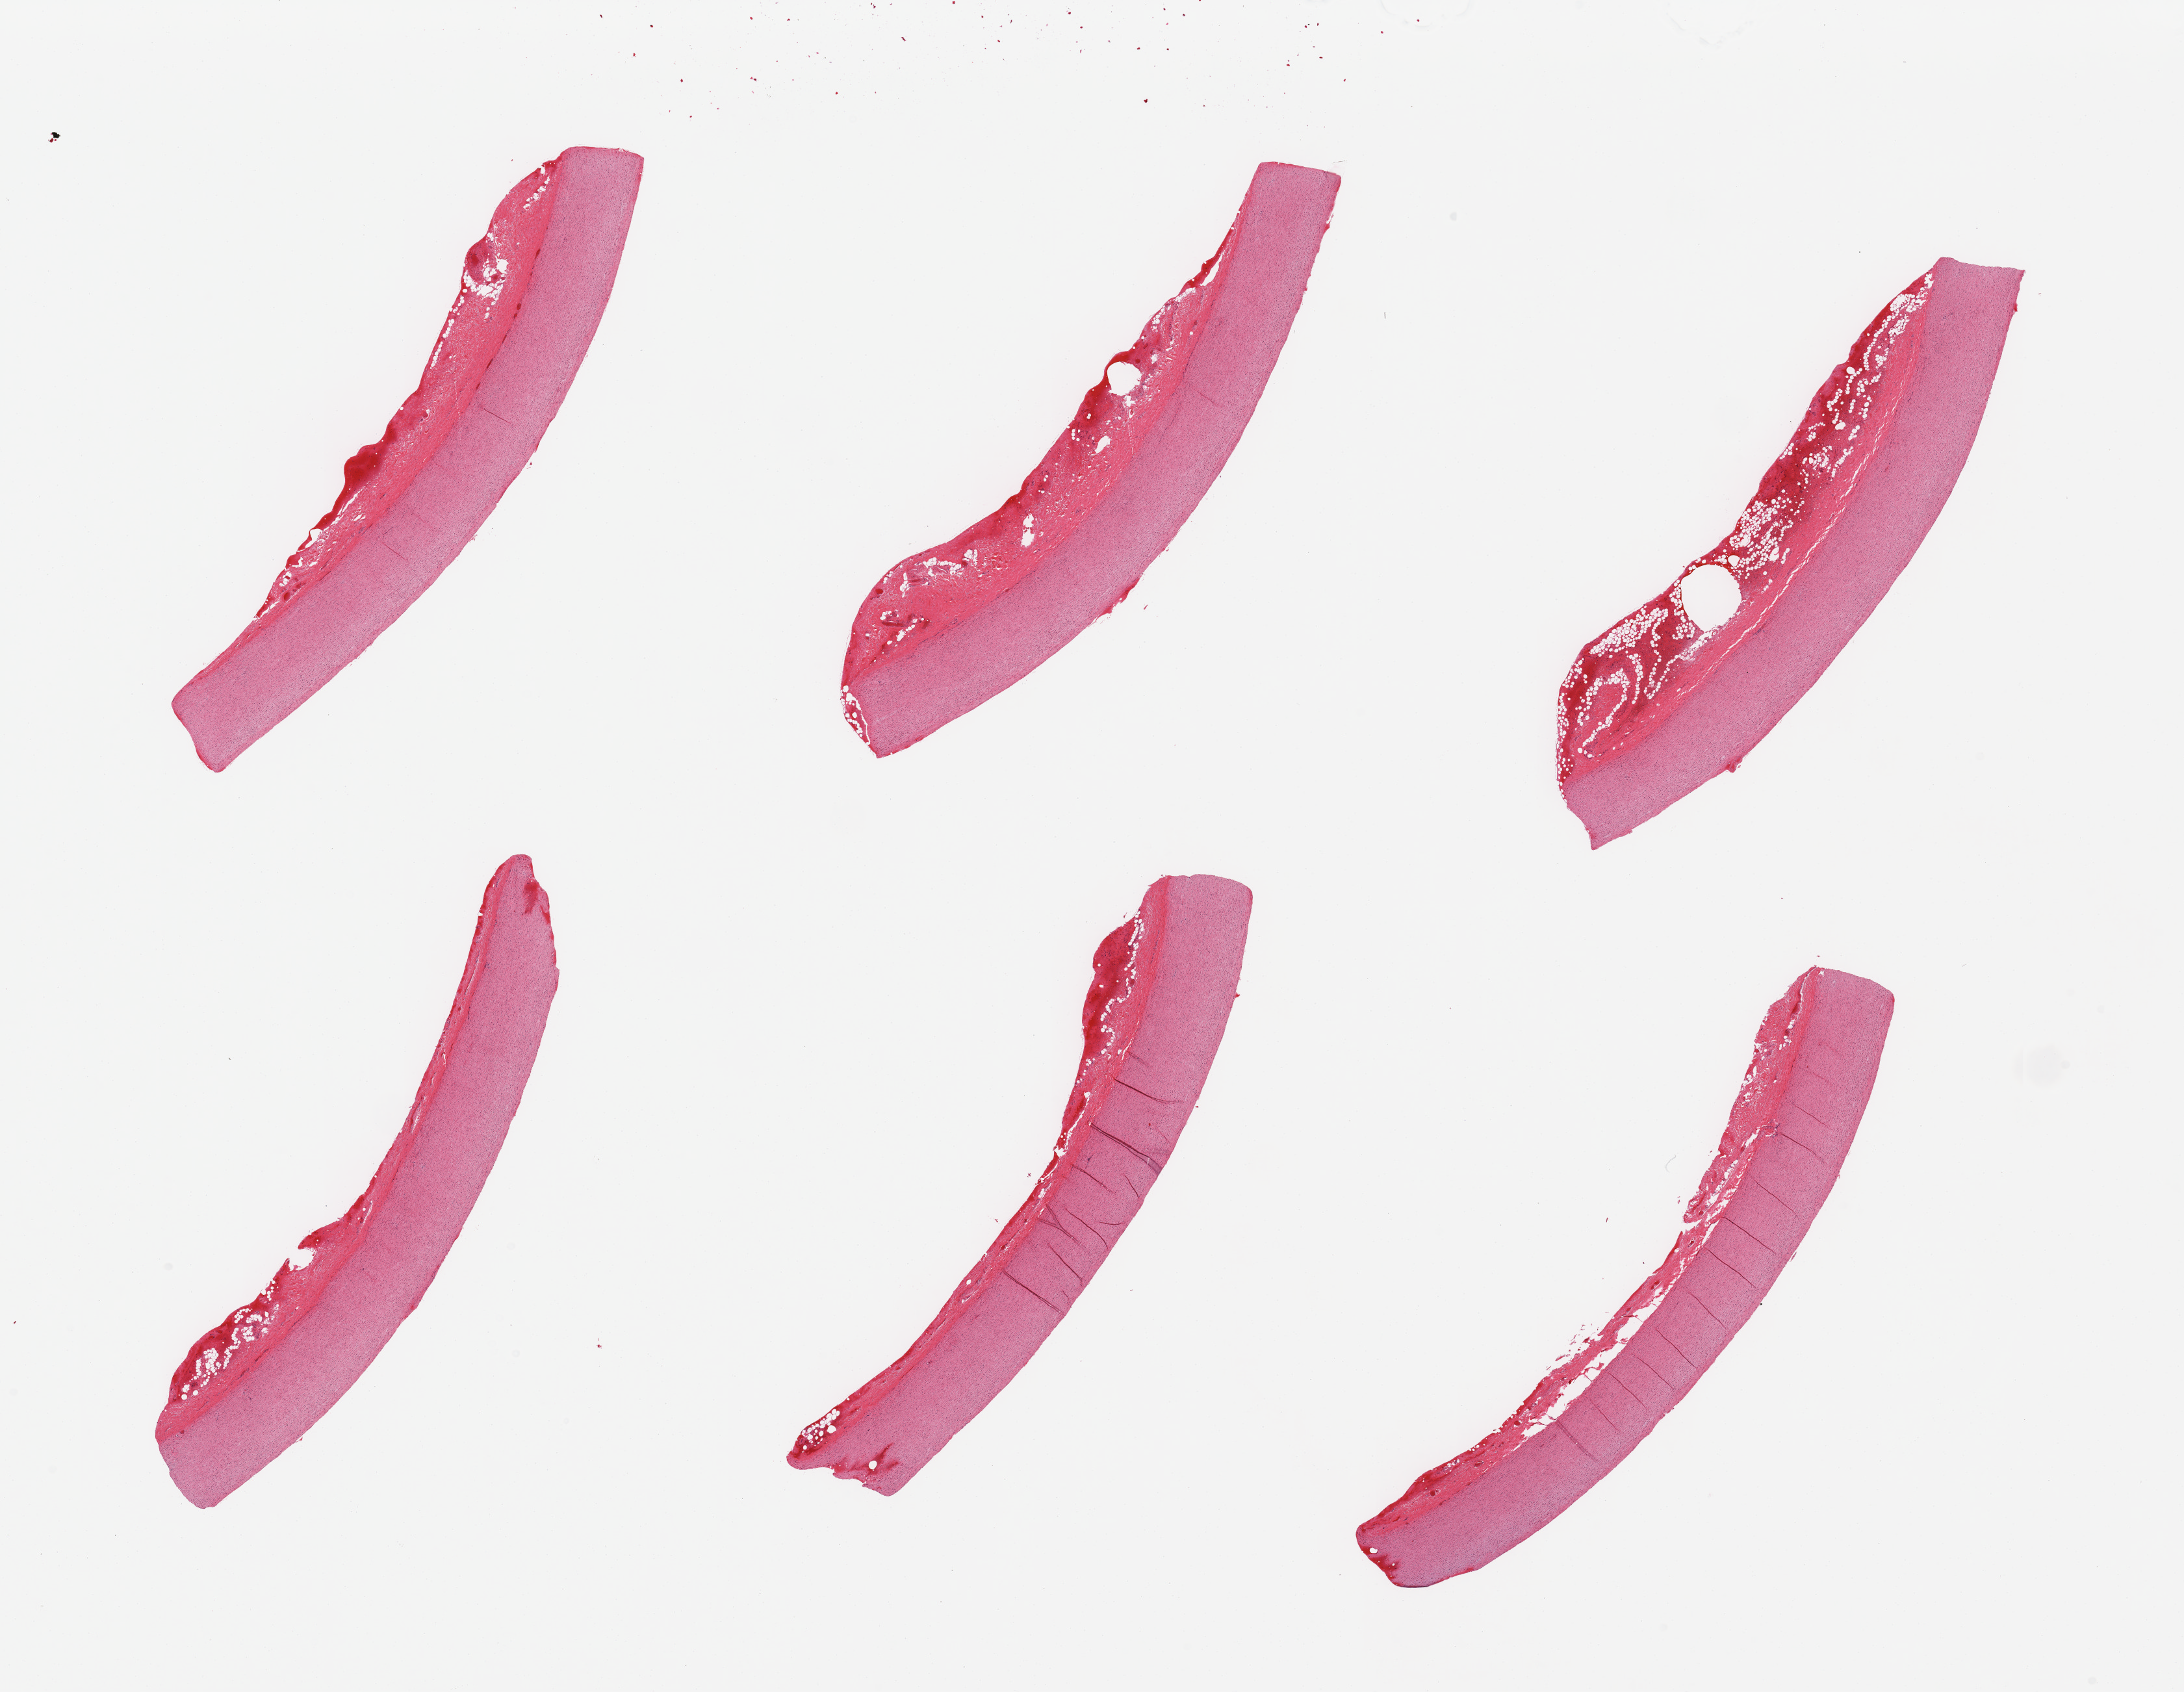
Digitized hematoxylin and eosin (H&E)-stained section — shown as a low-resolution overview of the whole scanned area (about 26.6 x 20.6 mm), PAXgene-fixed, paraffin-embedded tissue, target tissue: aorta, tissue donor sample. Donor sex: female.
Pathologist's review note for this sample: 6 pieces.